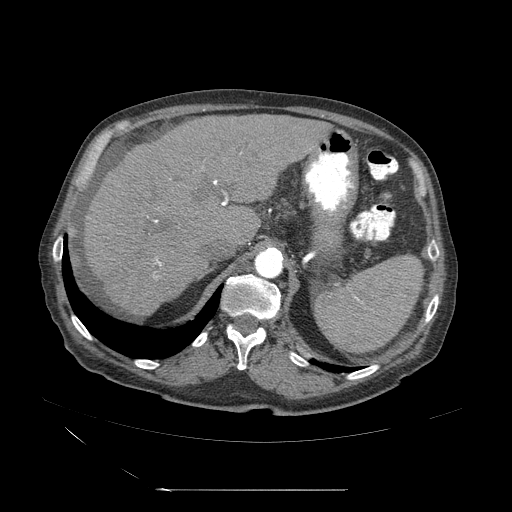
Contrast-enhanced abdominal CT (liver protocol), one axial slice. Slice 34 of 71 in the series (ordered by position). 120 kVp. Soft-tissue window (W 400 / L 40 HU). 512 × 512 image matrix, field of view 440 × 440 mm. From the clinical record (not read from this slice): diagnosis: hepatocellular carcinoma (patient treated with transarterial chemoembolisation; whether this scan precedes or follows treatment is not stated here); TNM stage (as recorded): Stage-II; Child-Pugh class: A; tumour nodularity: multinodular; tumour size: 1 cm.
Outlined on this slice (semi-automatic segmentation, software-assisted and operator-edited):
- abdominal aorta: bounding box <254,248,283,278> (left, top, right, bottom; pixels)
- liver parenchyma outside the tumour (the mass and vessels are separate outlines, so this box may not span the whole liver): <78,116,333,322>
- liver vessels: <139,161,236,291>